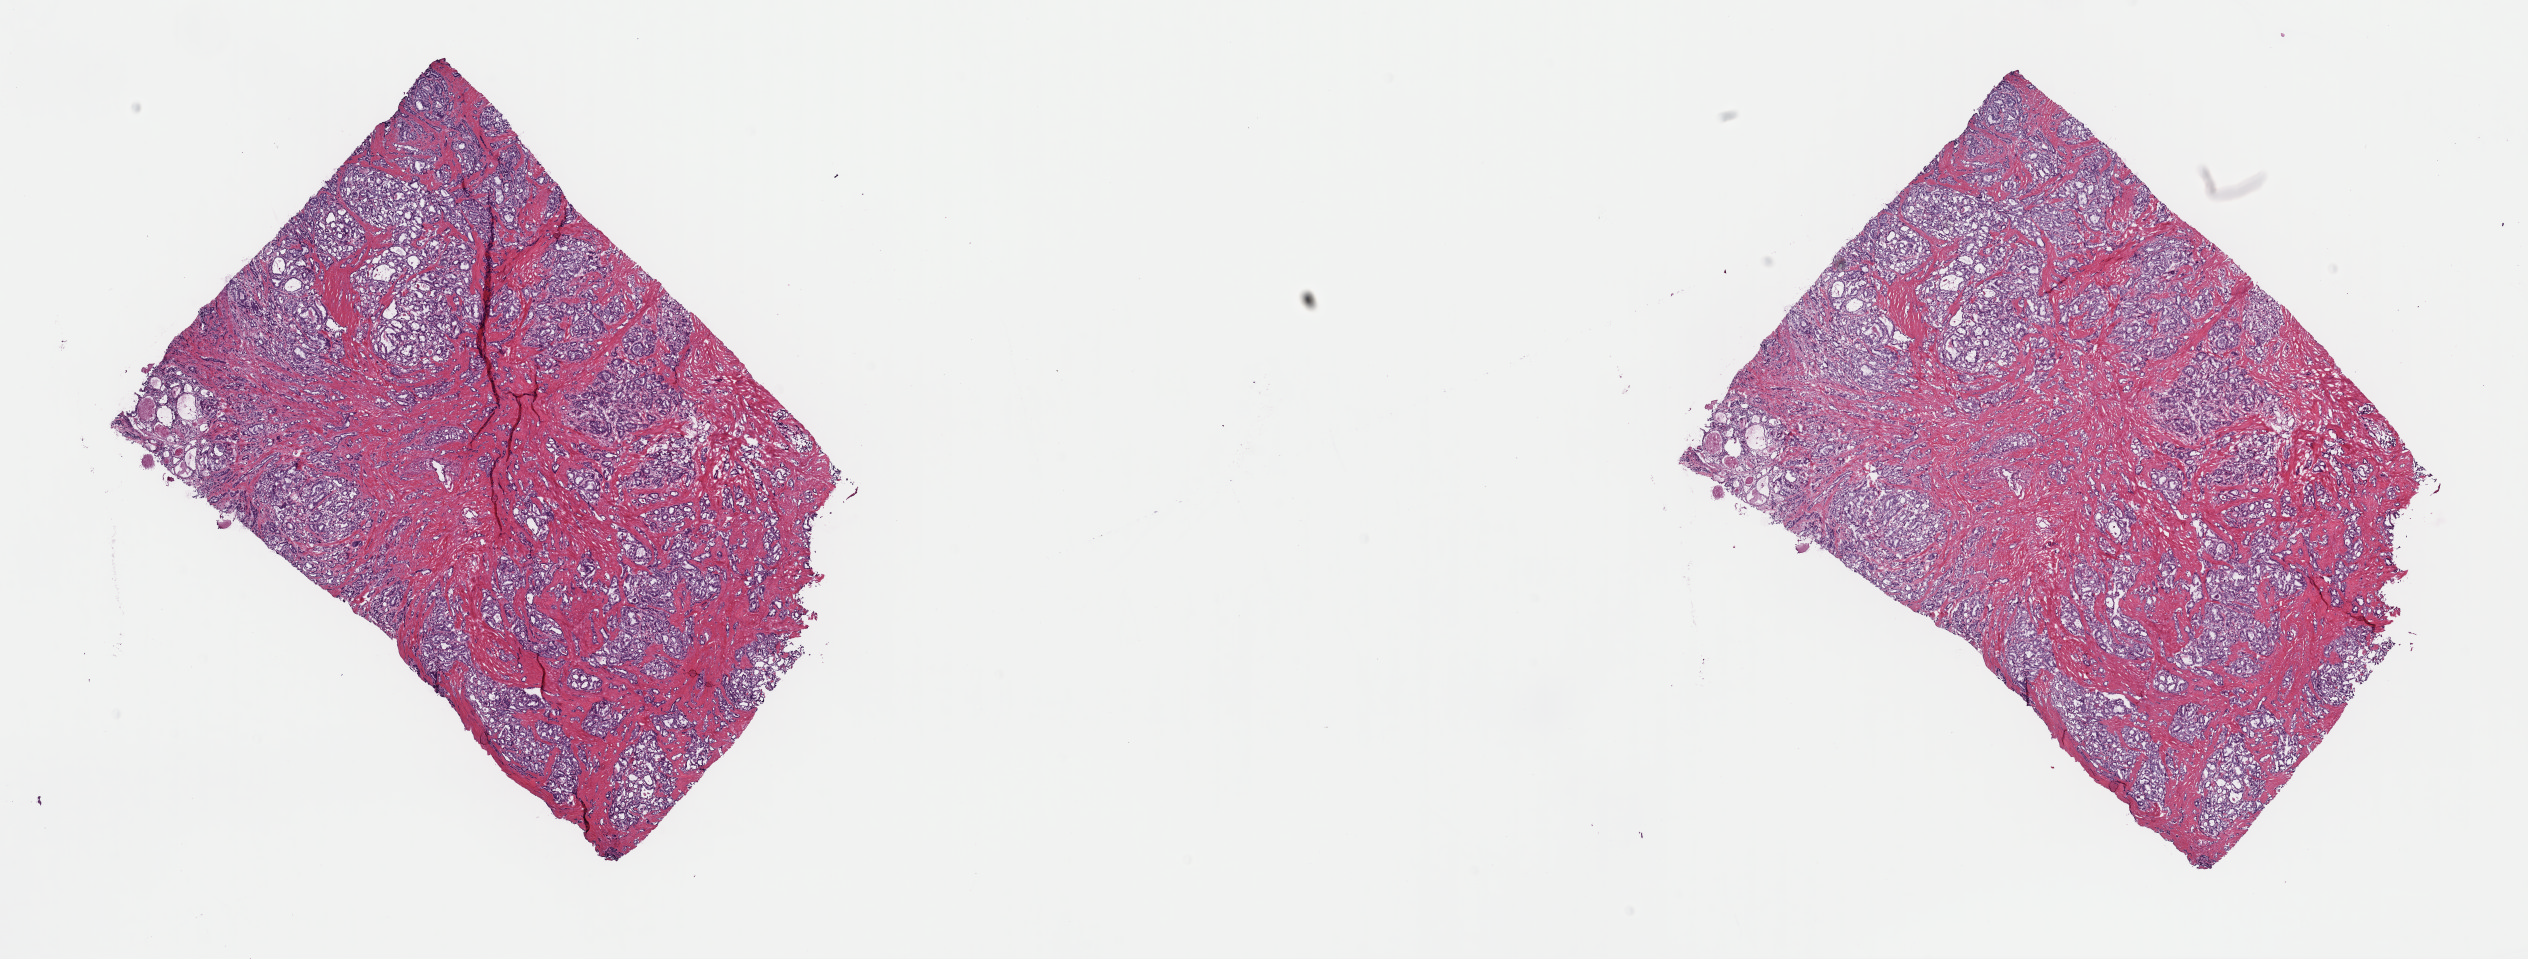
Digitized H&E-stained tissue section (whole slide) — shown as a low-resolution overview of the whole scanned area (about 20.0 x 7.6 mm, from a 40x scan). Frozen section from the top of the tissue portion. Thyroid, primary tumour sample. Female, age 49 years at initial diagnosis. Composition of this section per pathologist review: tumour cells 80%, tumour nuclei 80%, normal cells 0%, stromal cells 20%, necrosis 0%. Inflammatory infiltration, as recorded: lymphocyte infiltration 3%, monocyte infiltration 1%, neutrophil infiltration 1%.
Lymph nodes positive (case pathology): 0 of 2 examined. Histologic diagnosis: Papillary adenocarcinoma, NOS. Laterality: right. AJCC pathologic stage: III (7th edition).